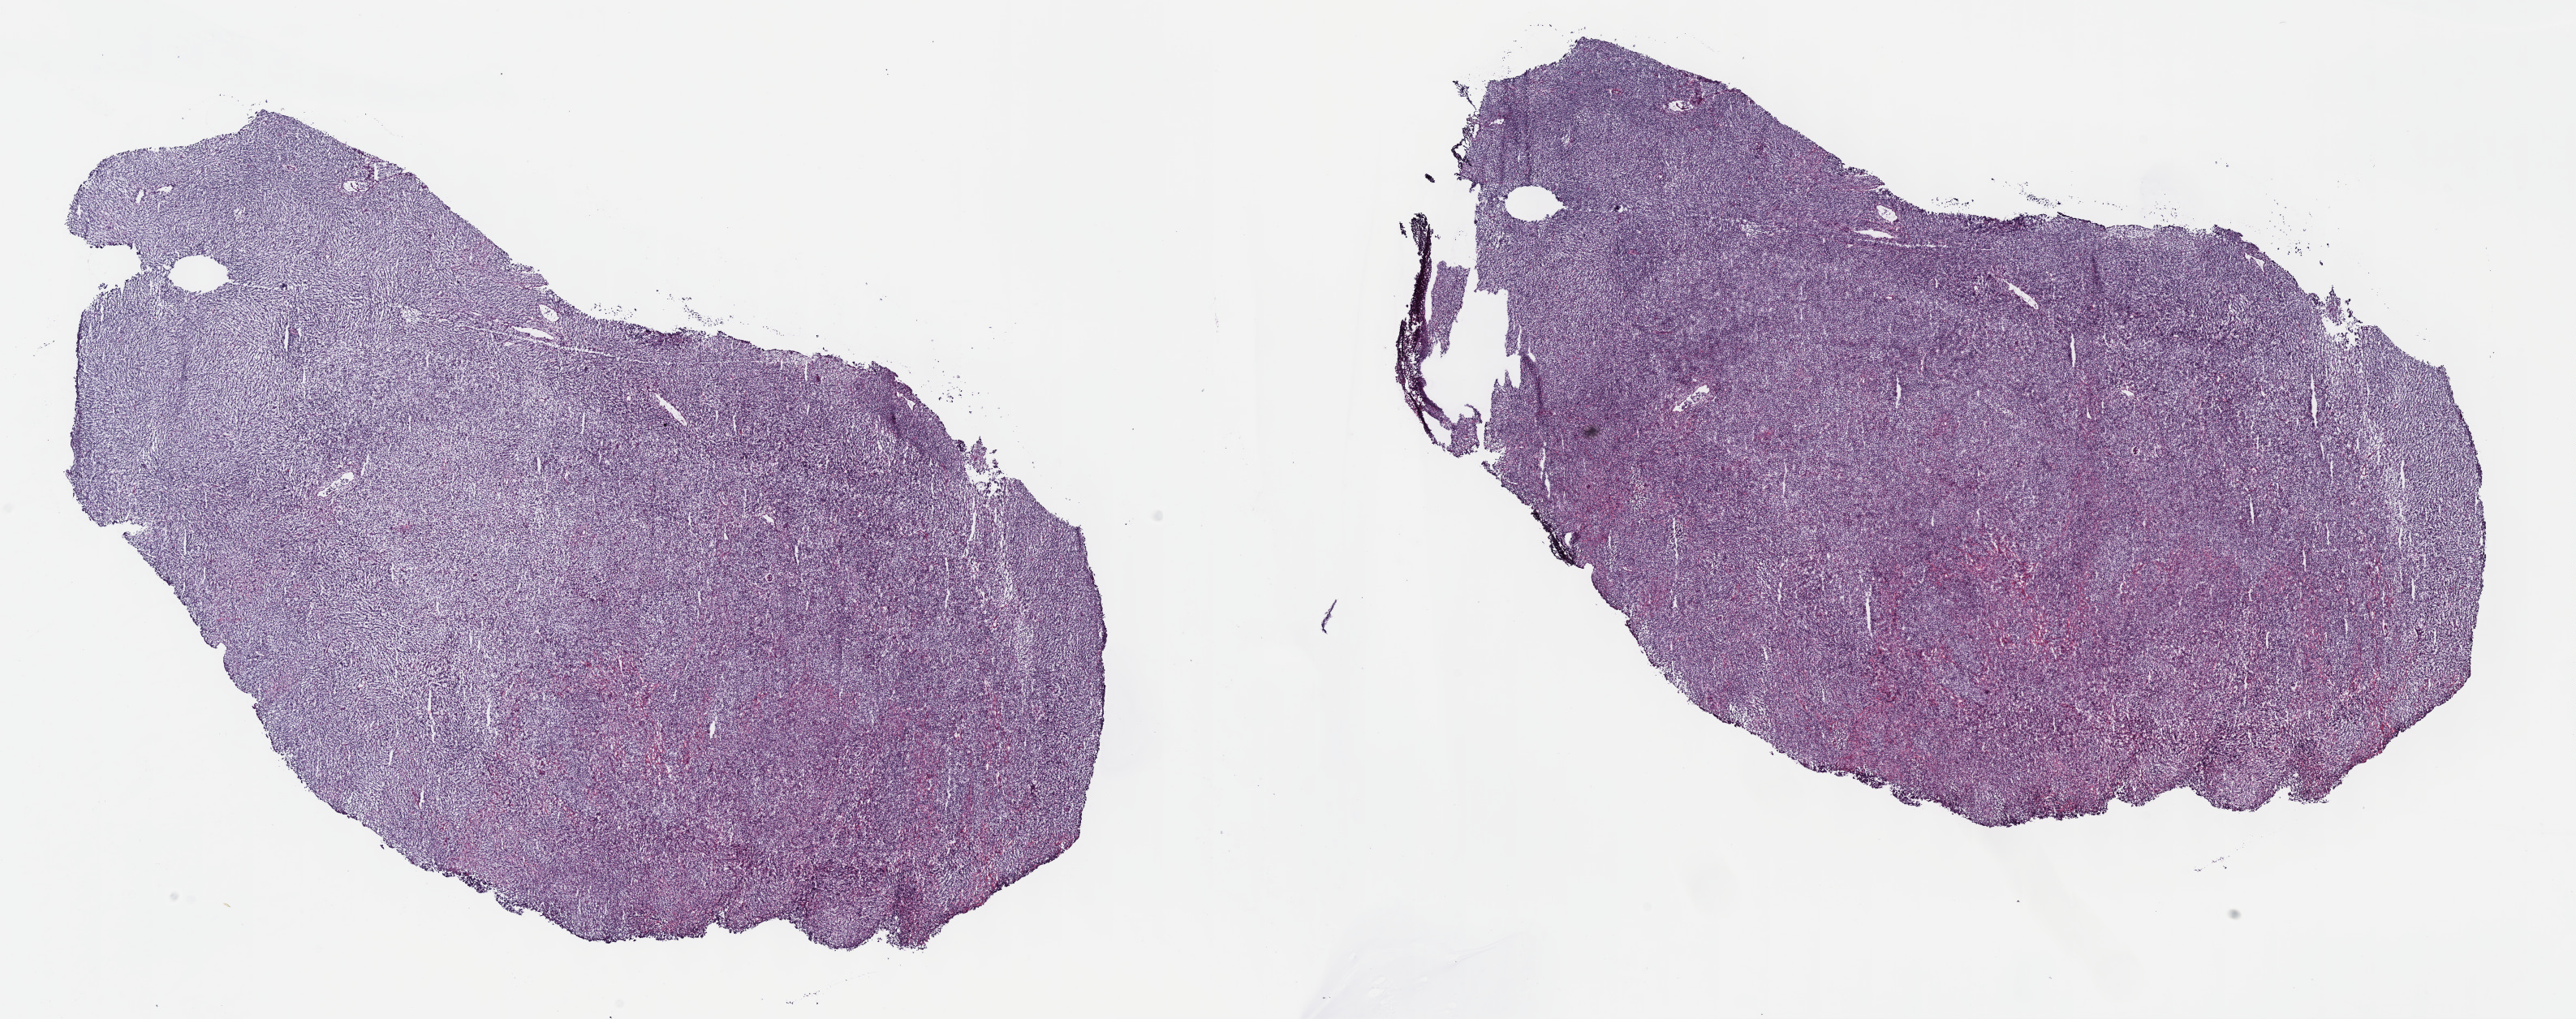
Whole-slide histology image, H&E, low-resolution overview of the scanned area, about 25.7 x 10.2 mm (from a 40x scan), frozen section, primary tumour sample from the lymphoid tissue. Female patient; age at initial diagnosis 77 years. Pathologist review of this section (percent, as recorded): tumour cells 95%, tumour nuclei 95%, normal cells 0%, stromal cells 5%, necrosis 0%. Infiltration values recorded for this section: lymphocyte infiltration 95%, monocyte infiltration 2%, neutrophil infiltration 0%.
Pathologic diagnosis: Diffuse large B-cell lymphoma, NOS (lymph nodes of inguinal region or leg).